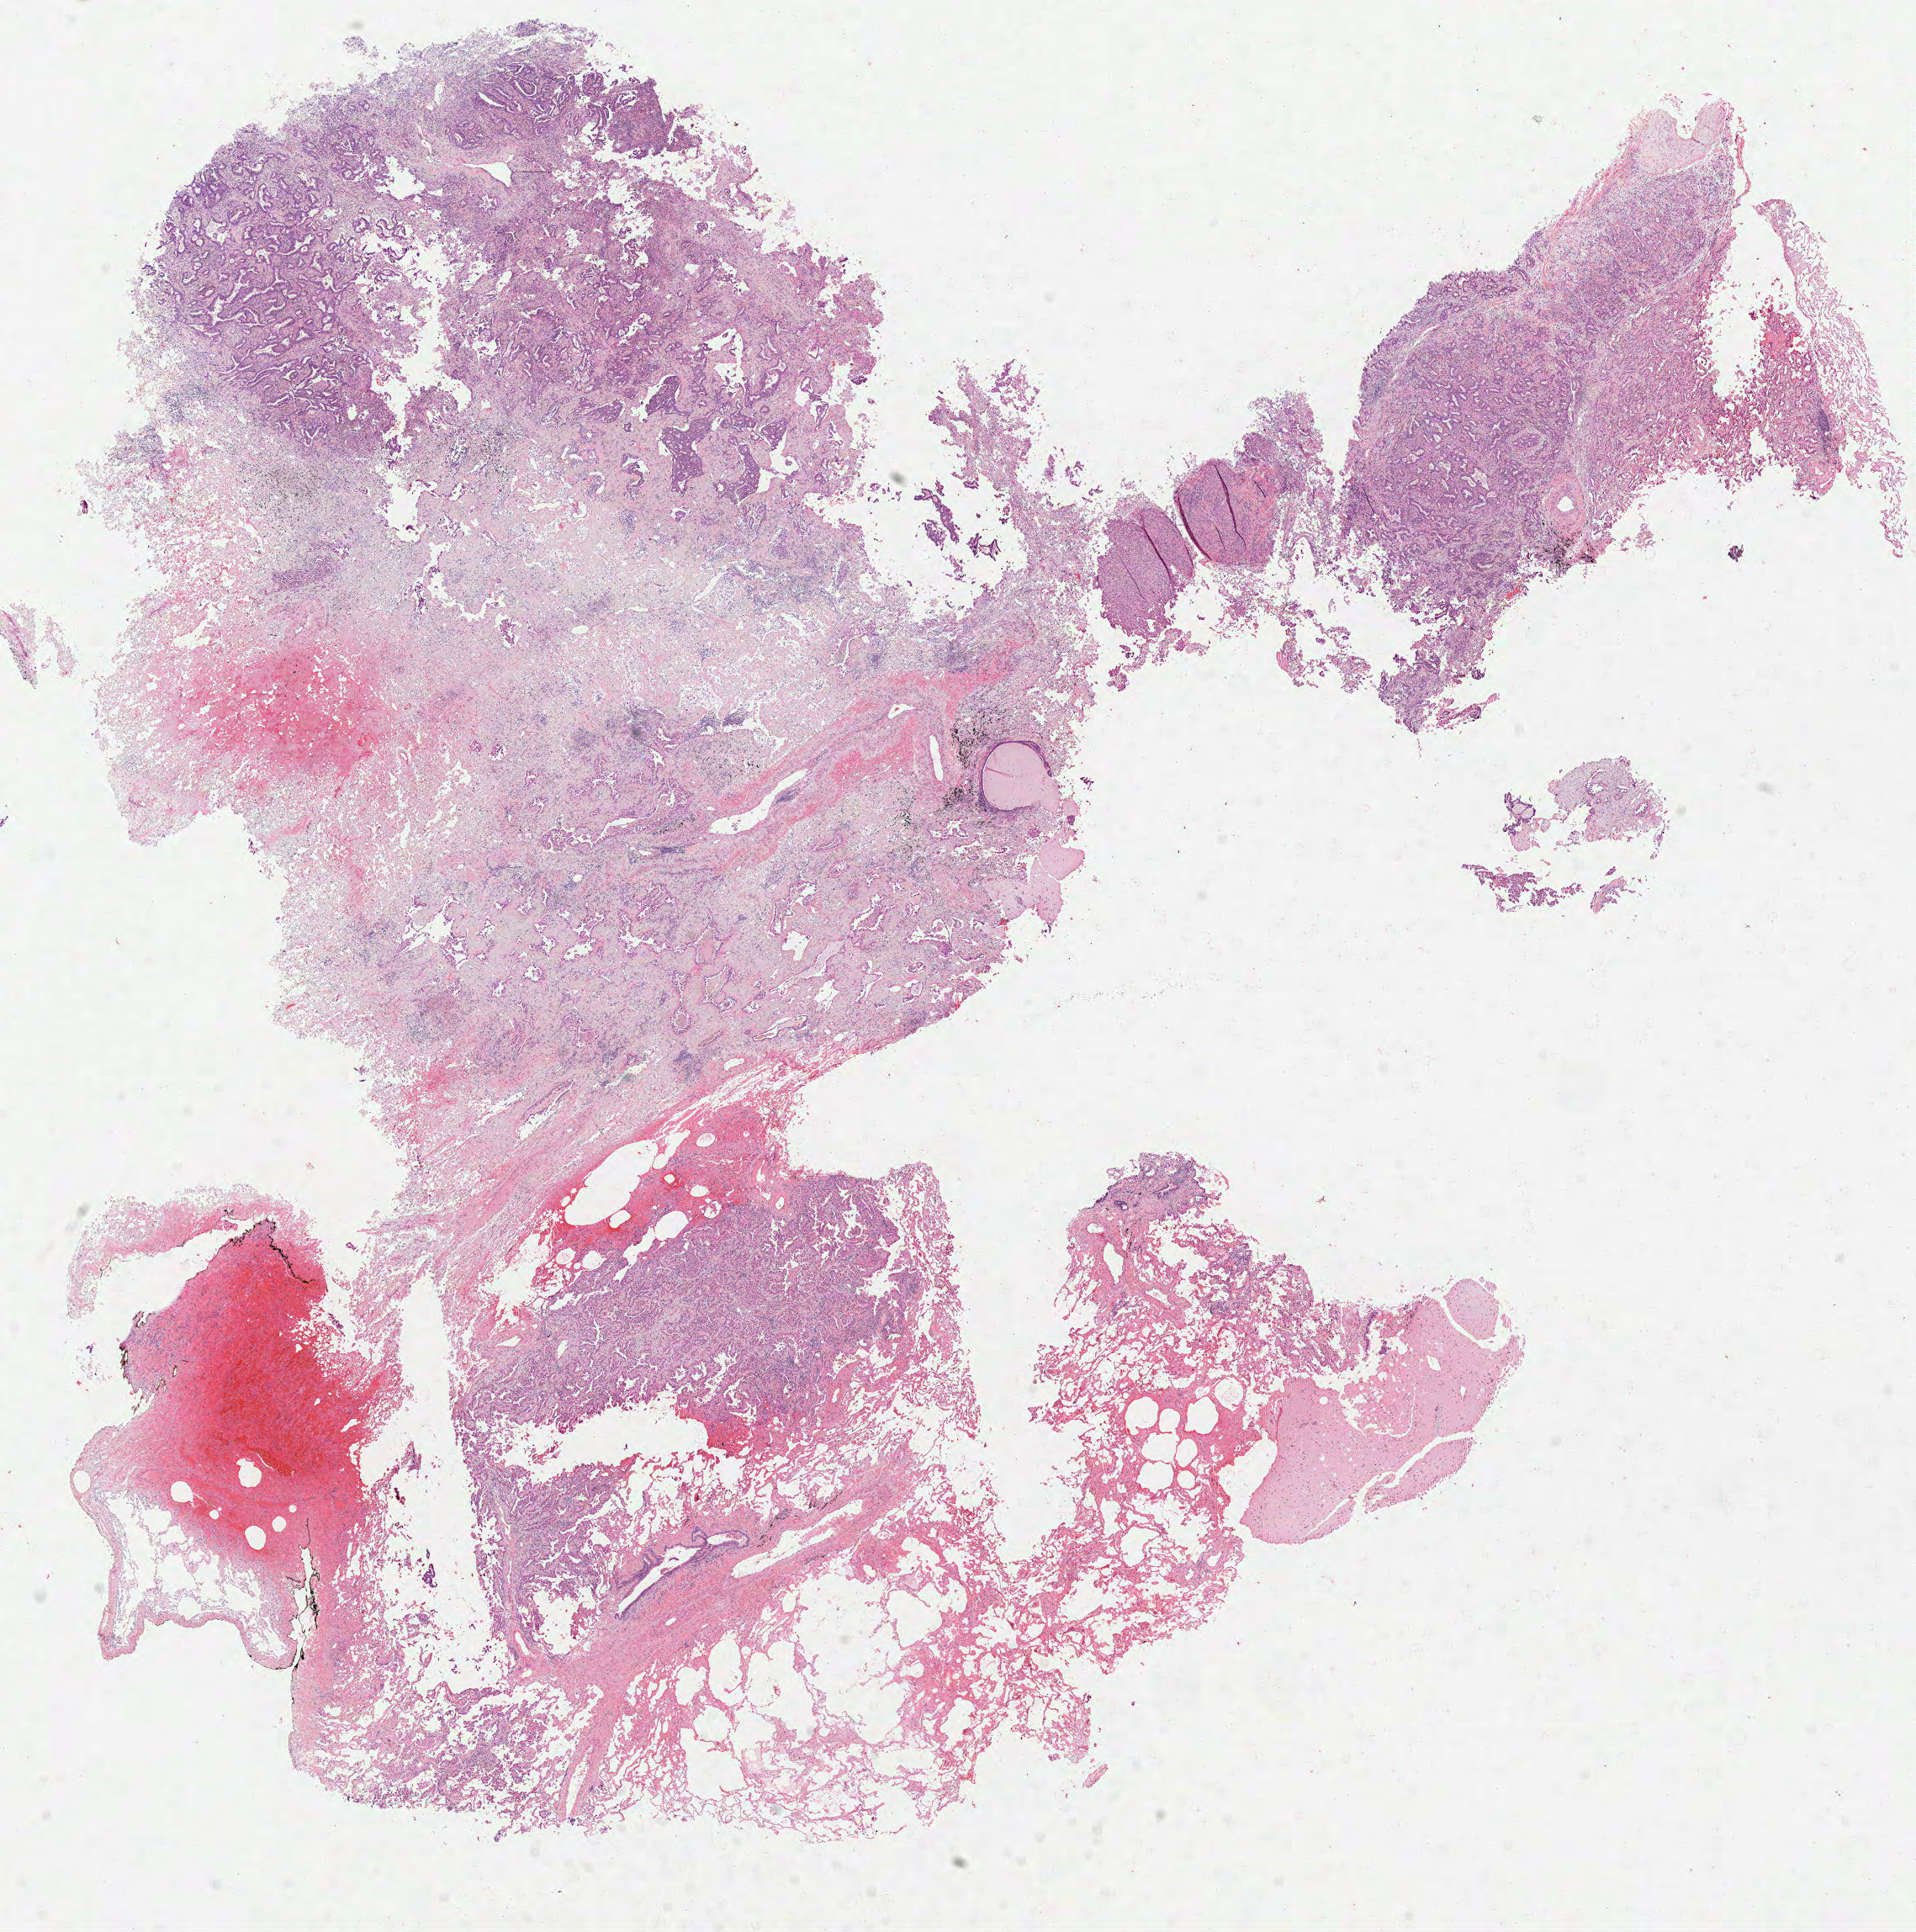
H&E whole-slide image, low-resolution overview of the scanned area, about 18.4 x 18.5 mm; formalin-fixed paraffin-embedded (FFPE) diagnostic section; lung, primary tumour sample. Female patient; age at initial diagnosis 81 years.
AJCC pathologic stage: IB (7th edition). Diagnosis: Adenocarcinoma with mixed subtypes (upper lobe, lung). TNM: T2a N0 M0.